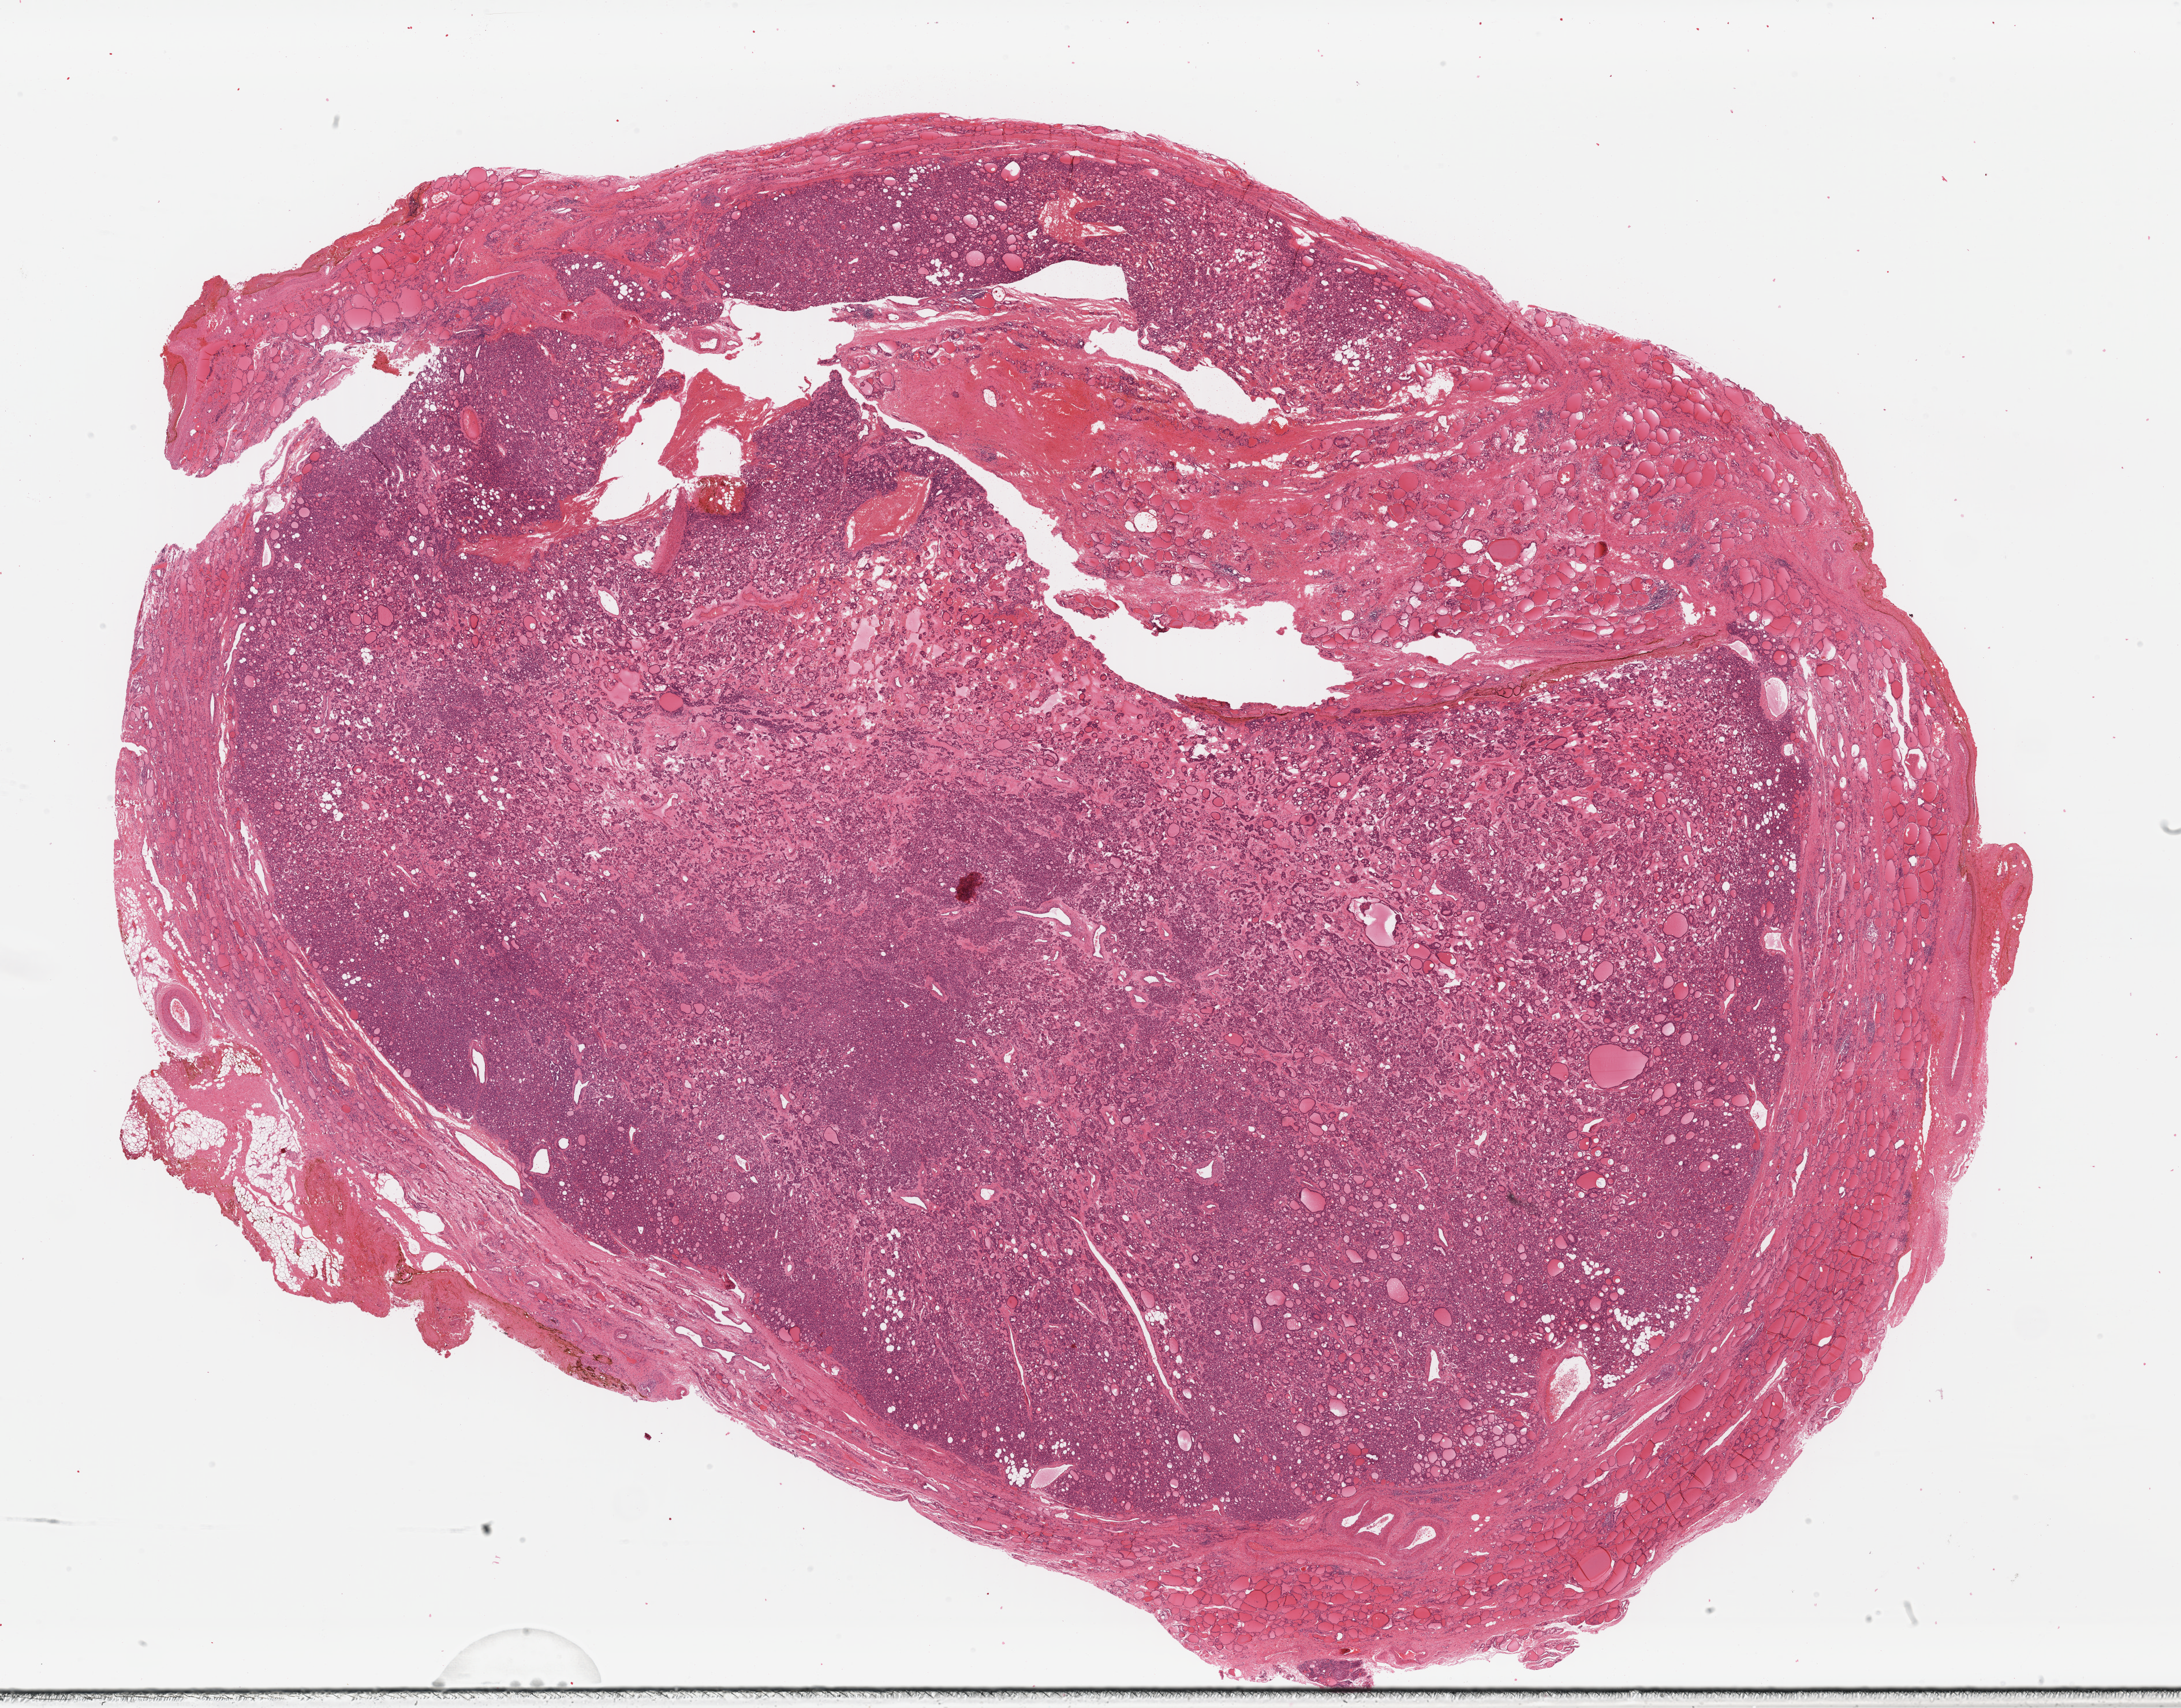
Digitized Hematoxylin and eosin (H&E) stained tissue section (whole slide), low-resolution overview of the scanned area, about 29.8 x 23.3 mm. FFPE section. Thyroid, primary tumour sample. Female patient; age at initial diagnosis 53 years.
• pathologic diagnosis: Papillary carcinoma, follicular variant (thyroid gland)
• AJCC pathologic stage: II
• lymph nodes positive (case pathology): 0 of 5 examined